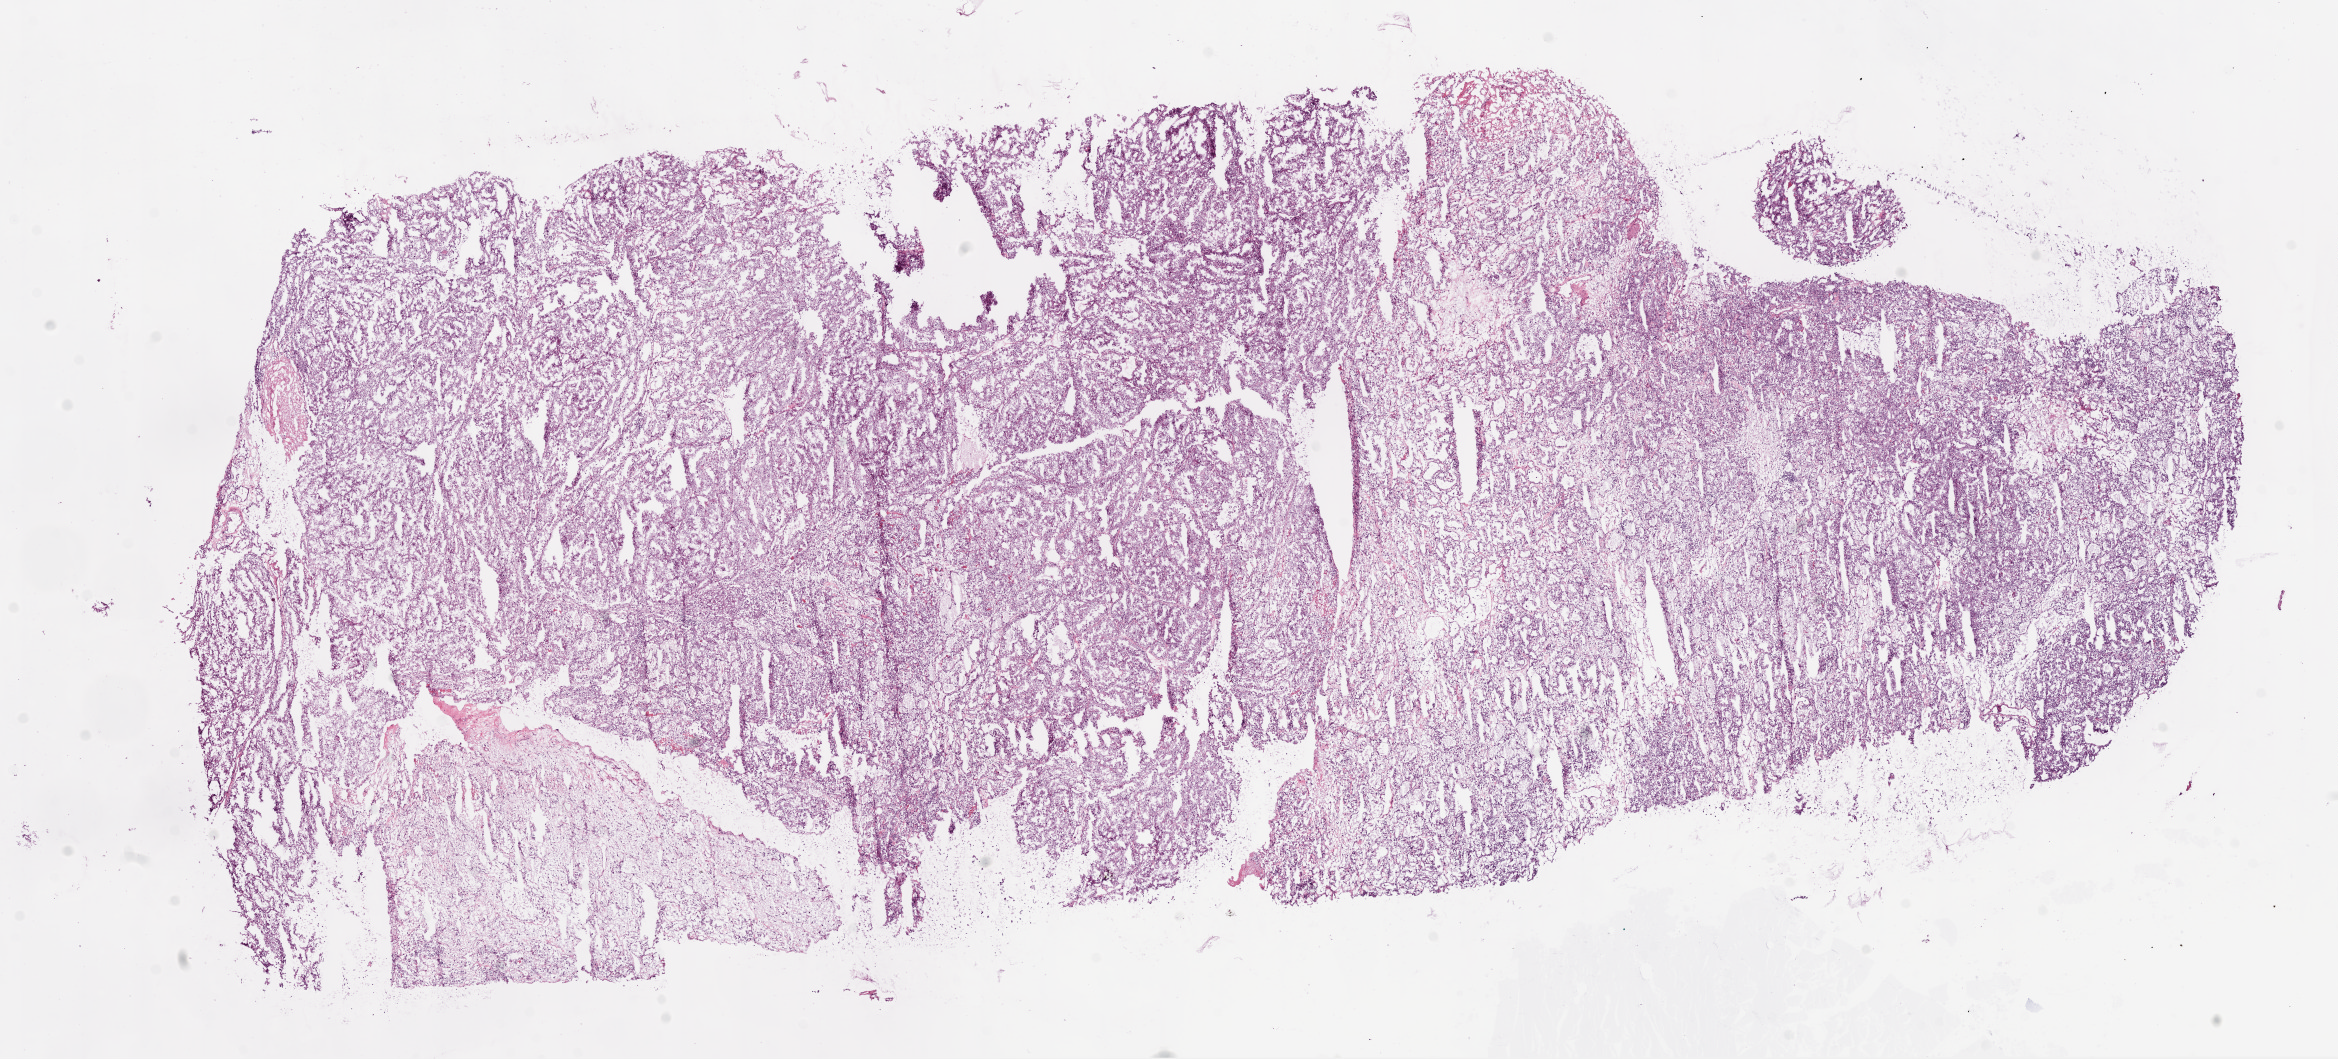
H&E-stained whole-slide image, whole scanned area (about 18.9 x 8.5 mm) shown as a low-resolution overview, frozen section from the top of the tissue portion, sample: primary tumour, kidney. Male patient. Histologic grade: G3 (poorly differentiated). Slide review estimates, as recorded: tumour cells 95%, tumour nuclei 80%, normal cells 0%, stromal cells 5%, necrosis 0%.
- histologic diagnosis: Clear cell adenocarcinoma, NOS
- AJCC pathologic stage: I